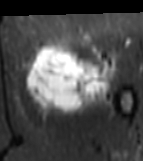
MRI of an extremity soft-tissue mass, one axial slice; slice 27 of 81 in the series (ordered by position); STIR; MR volume resampled by the dataset authors to the PET/CT grid (not the native acquisition matrix); 3.27 mm slice thickness; 143 × 161 image matrix, field of view 140 × 157 mm. Female patient. Case-level facts recorded for this patient, not image findings: histological type: myxofibrosarcoma; grade: intermediate; site of the primary tumour: left thigh.
Outlined on this slice (expert contour drawn on MRI and transferred to this co-registered scan by the dataset authors):
- gross tumour volume including surrounding oedema: box from (x=24, y=42) to (x=116, y=116) px
- gross tumour volume (mass): (x=26, y=46)–(x=112, y=111)